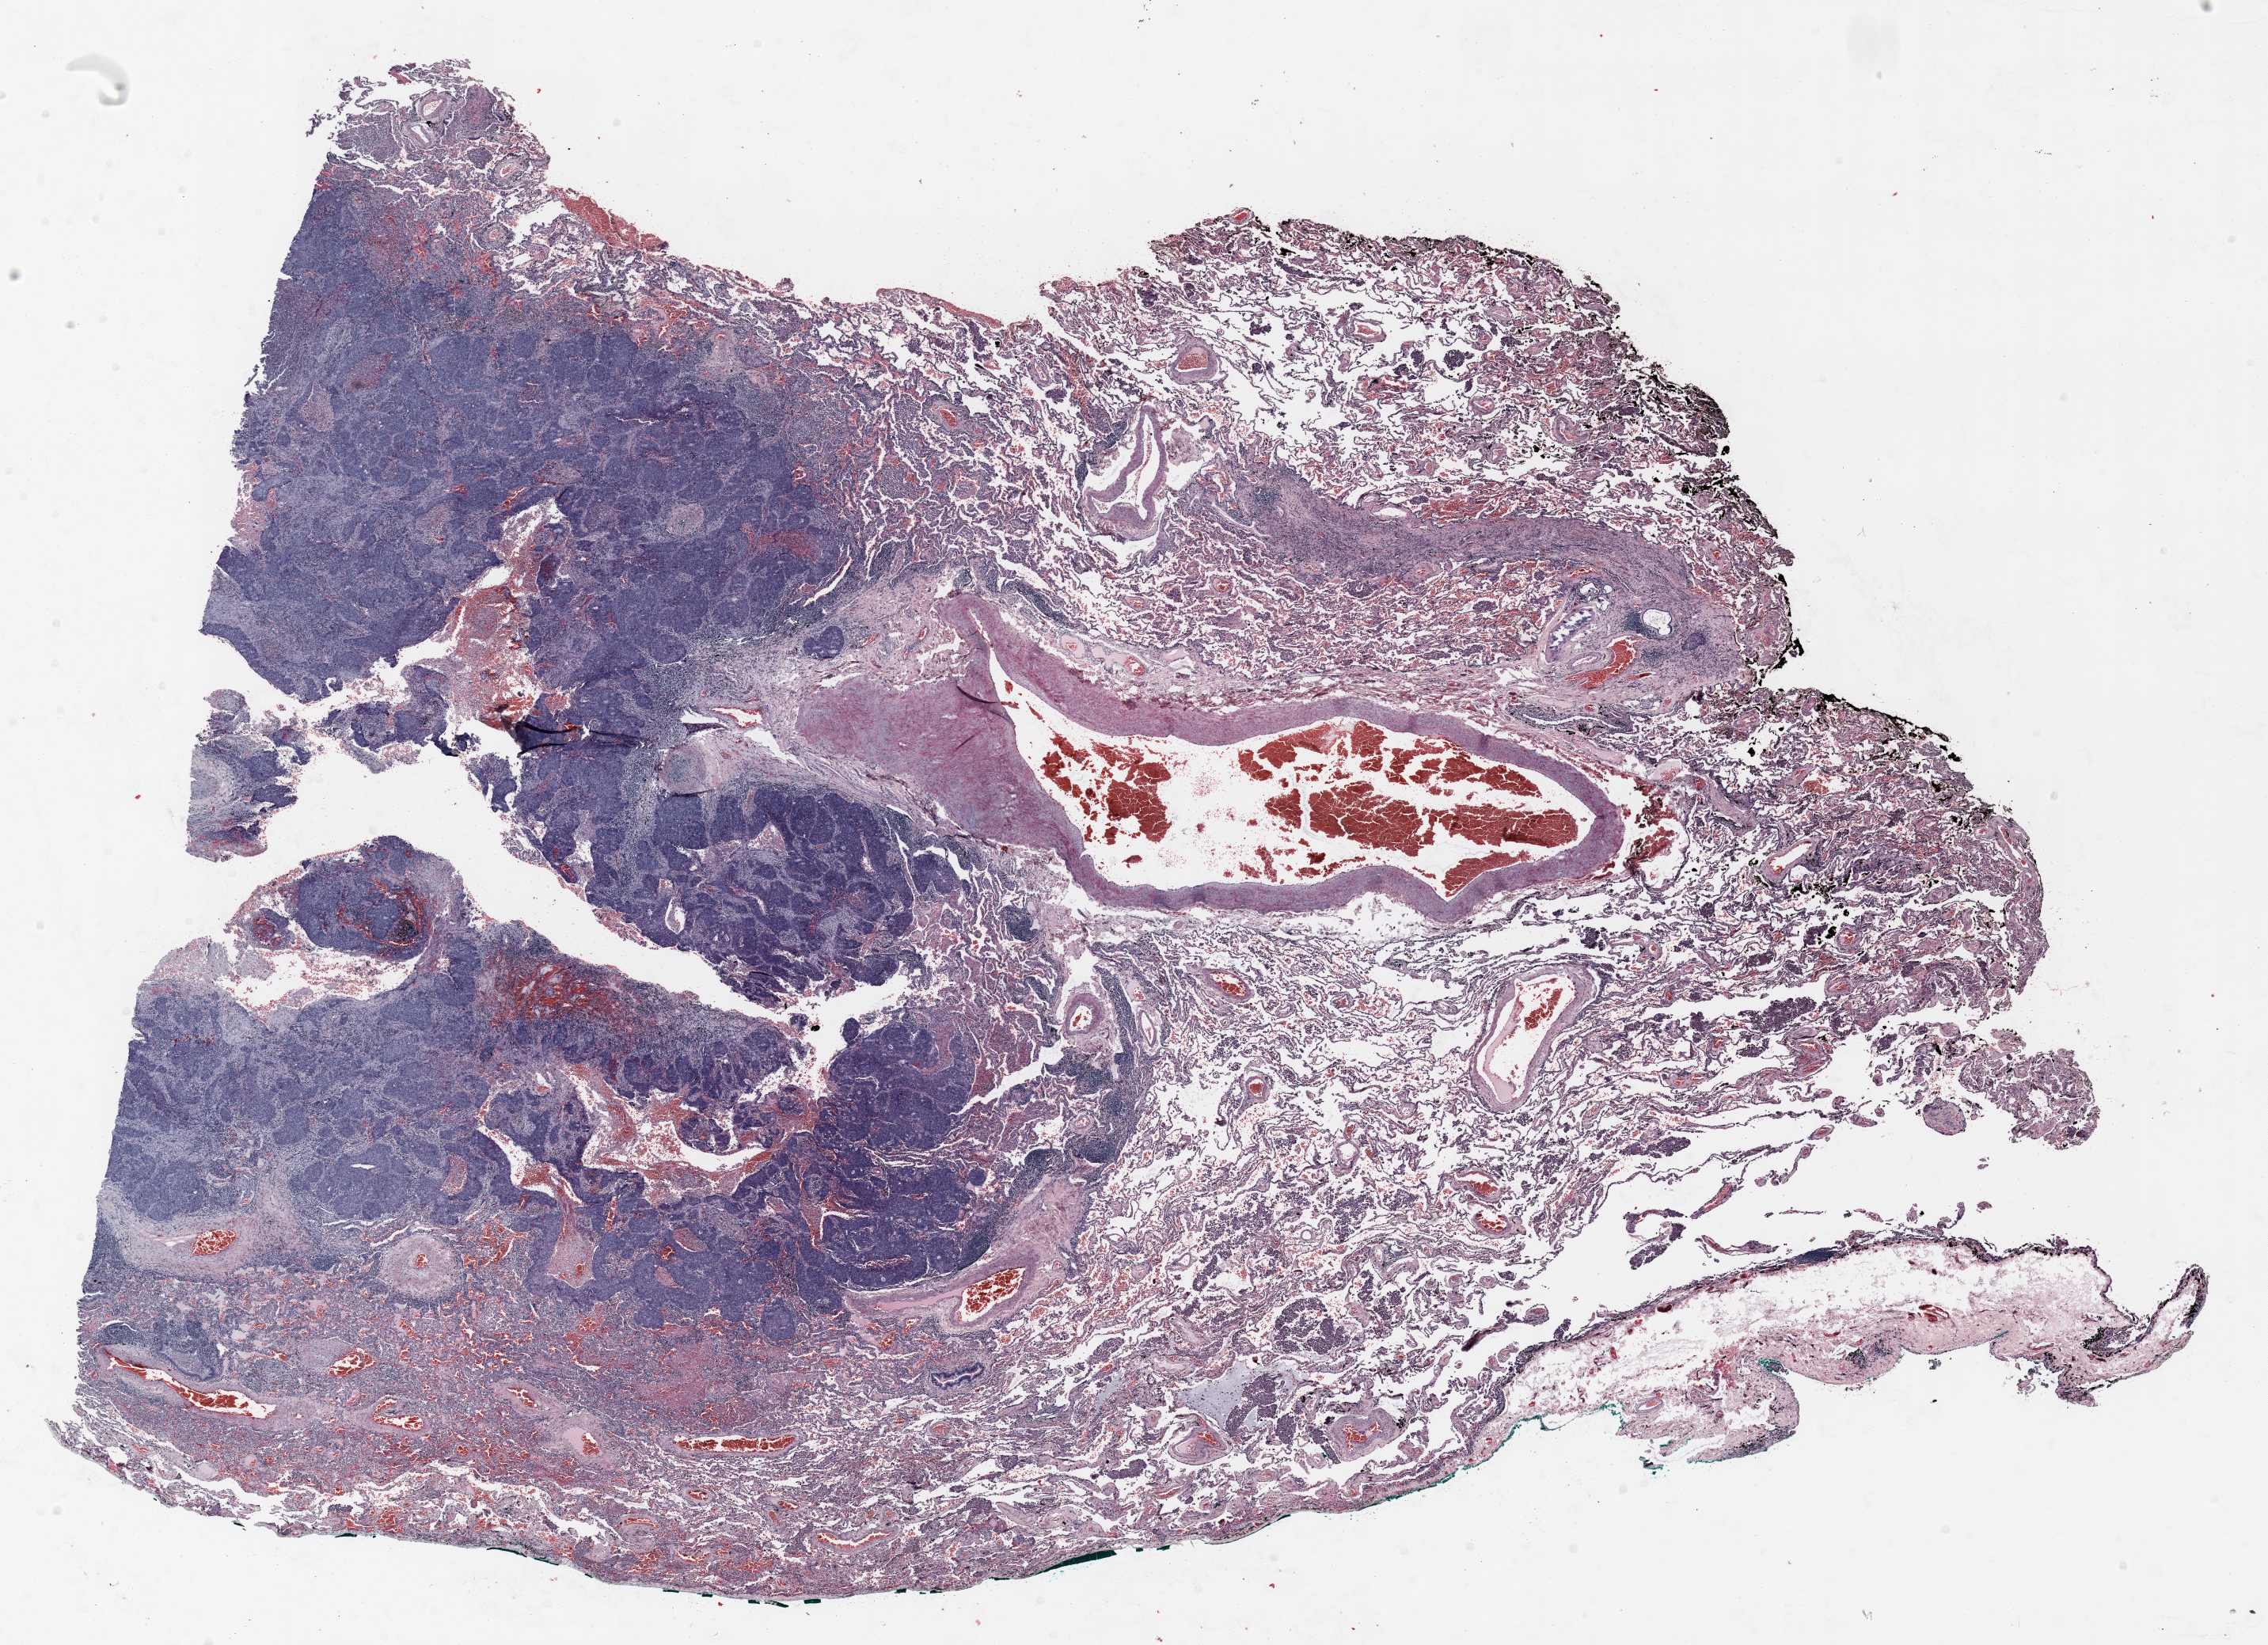
Whole-slide histology image, H&E — shown as a low-resolution overview of the whole scanned area (about 23.0 x 16.7 mm, slide scanned at 20x). FFPE section. Lung tissue. Male patient, aged 58 at enrolment. Grade: moderately differentiated (G2).
- primary tumour location (clinical record): right middle lobe
- tumour size (pathology): 24 mm
- stage (AJCC 6th edition): IA
- participant's lung-cancer diagnosis: Squamous cell carcinoma, NOS (ICD-O-3 8070/3)